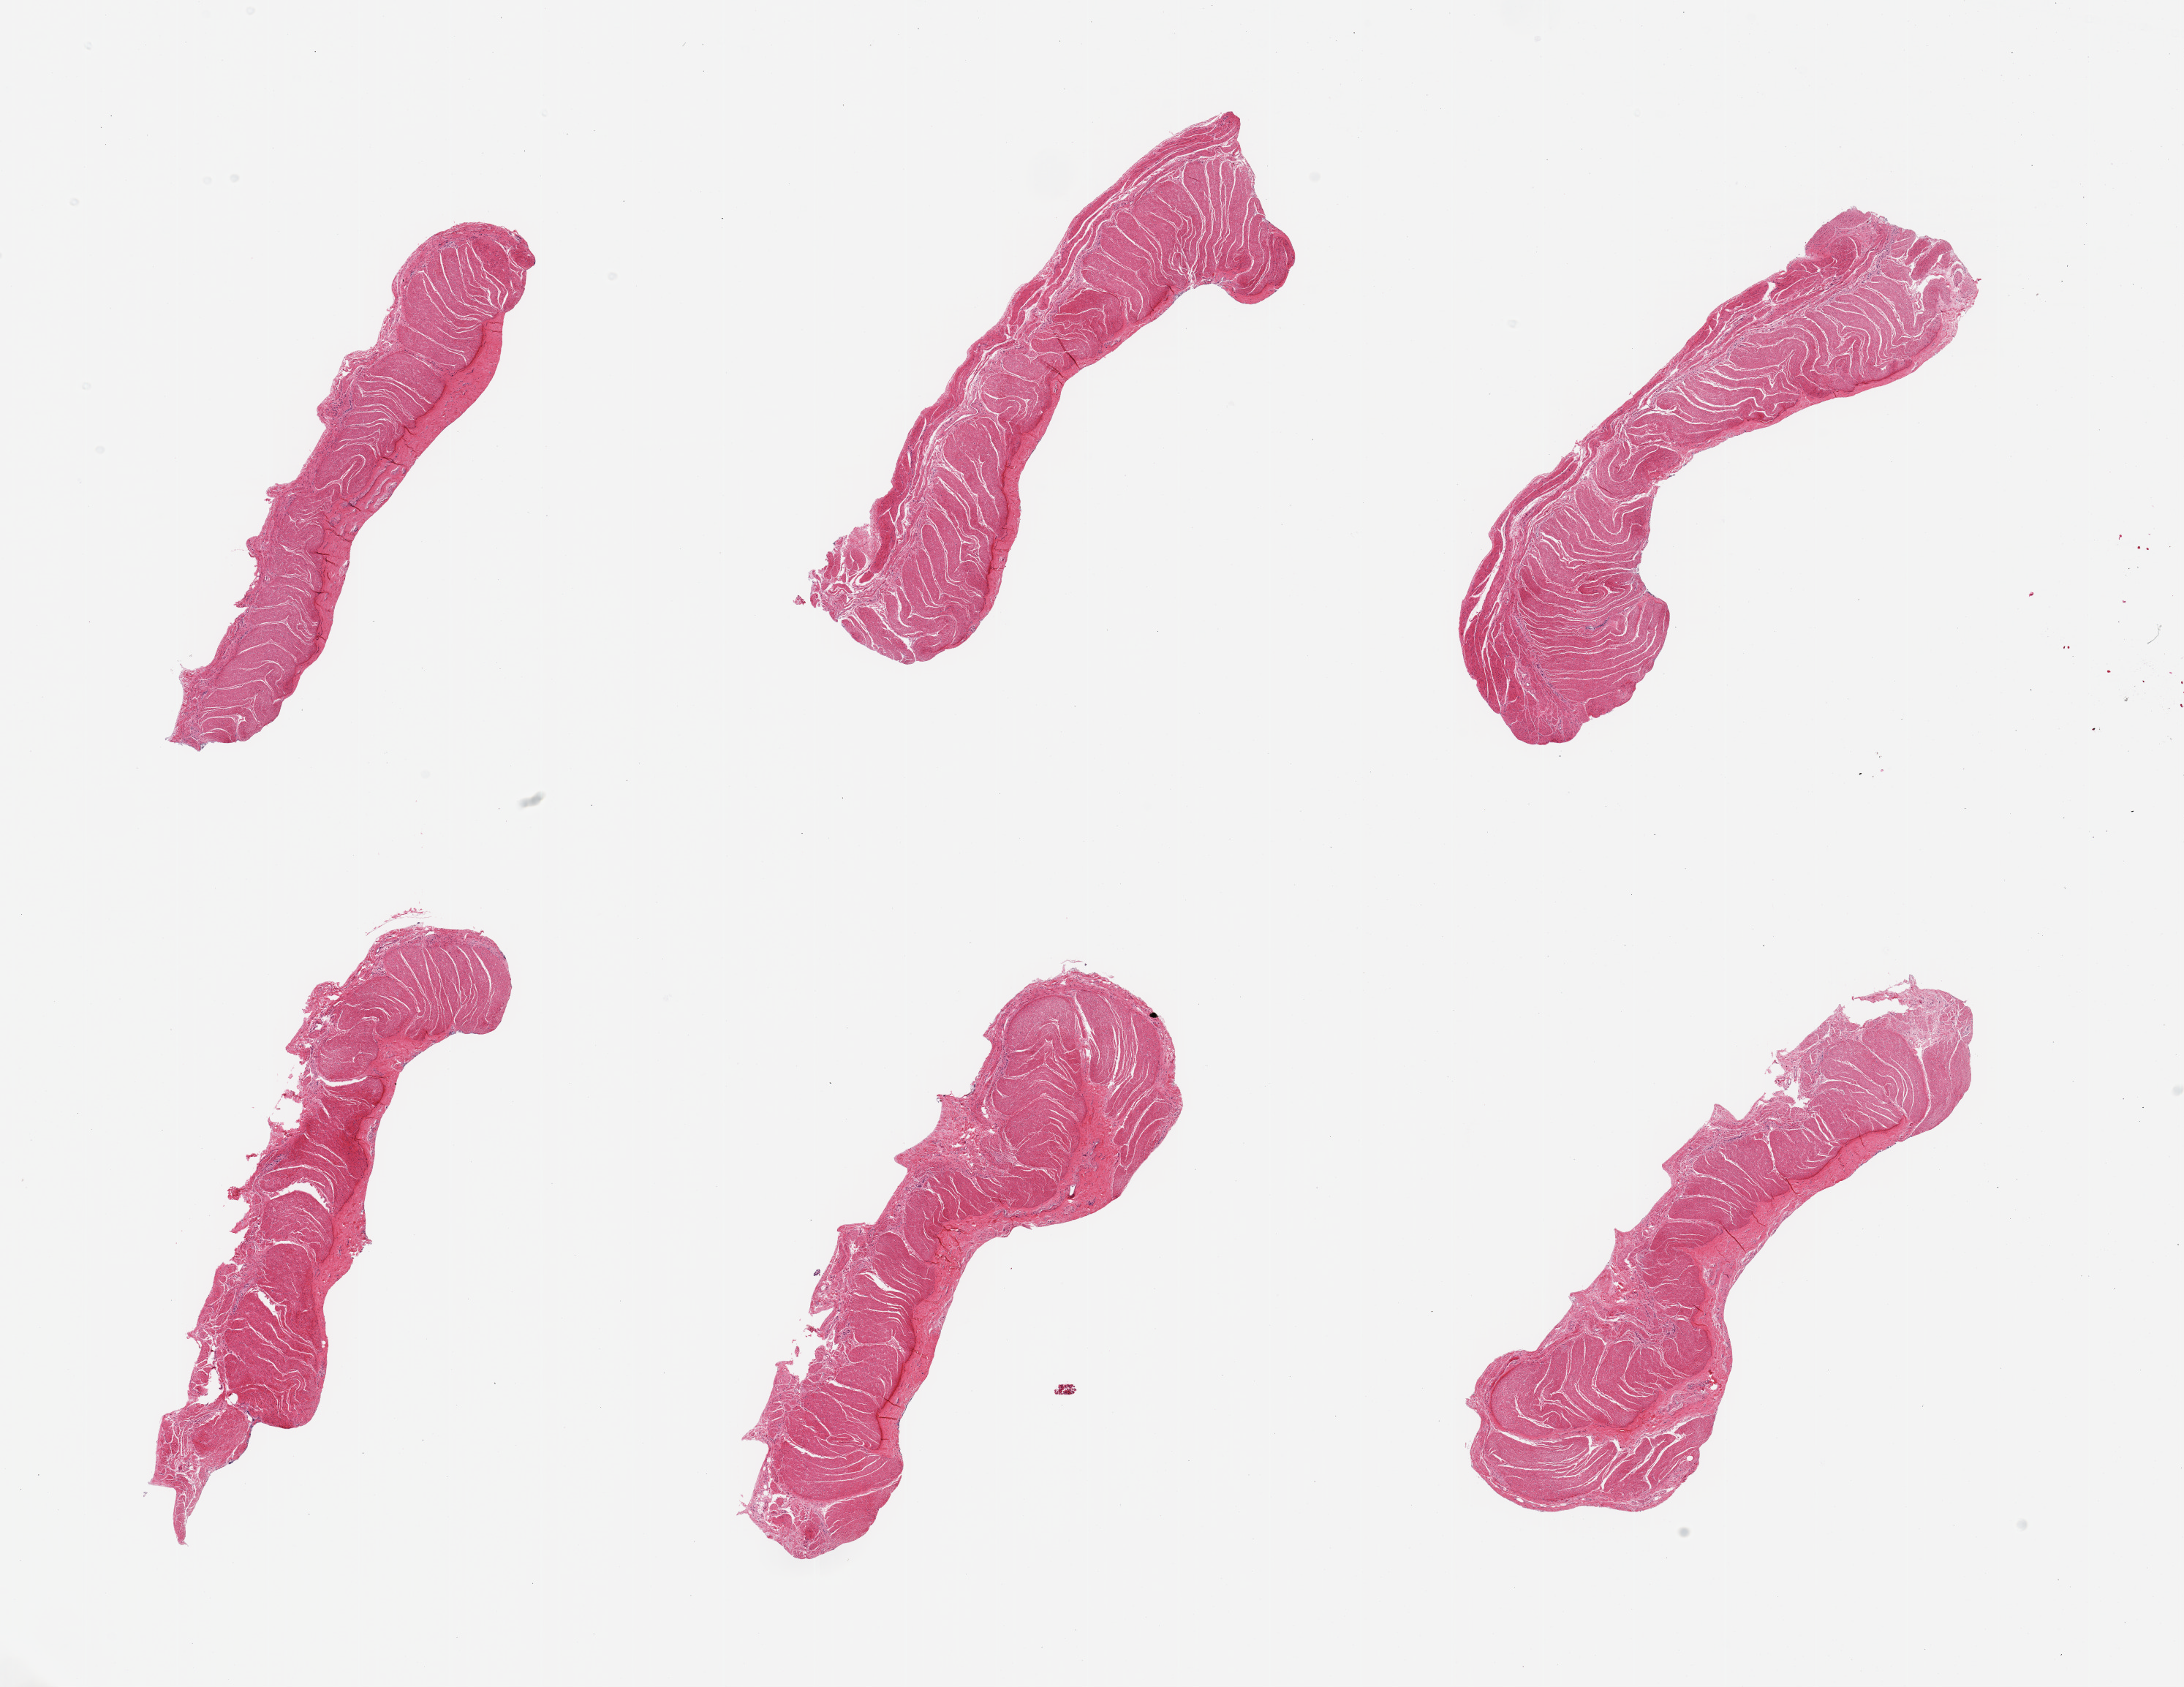
Digitized haematoxylin and eosin-stained section — low-resolution overview of the scanned area, about 23.6 x 18.2 mm (slide scanned at 20x). PAXgene-fixed paraffin-embedded (PFPE) section. Section of sigmoid colon (target tissue). Donor tissue sample. Donor: male.
• review note (as recorded): 6 pieces; target muscularis